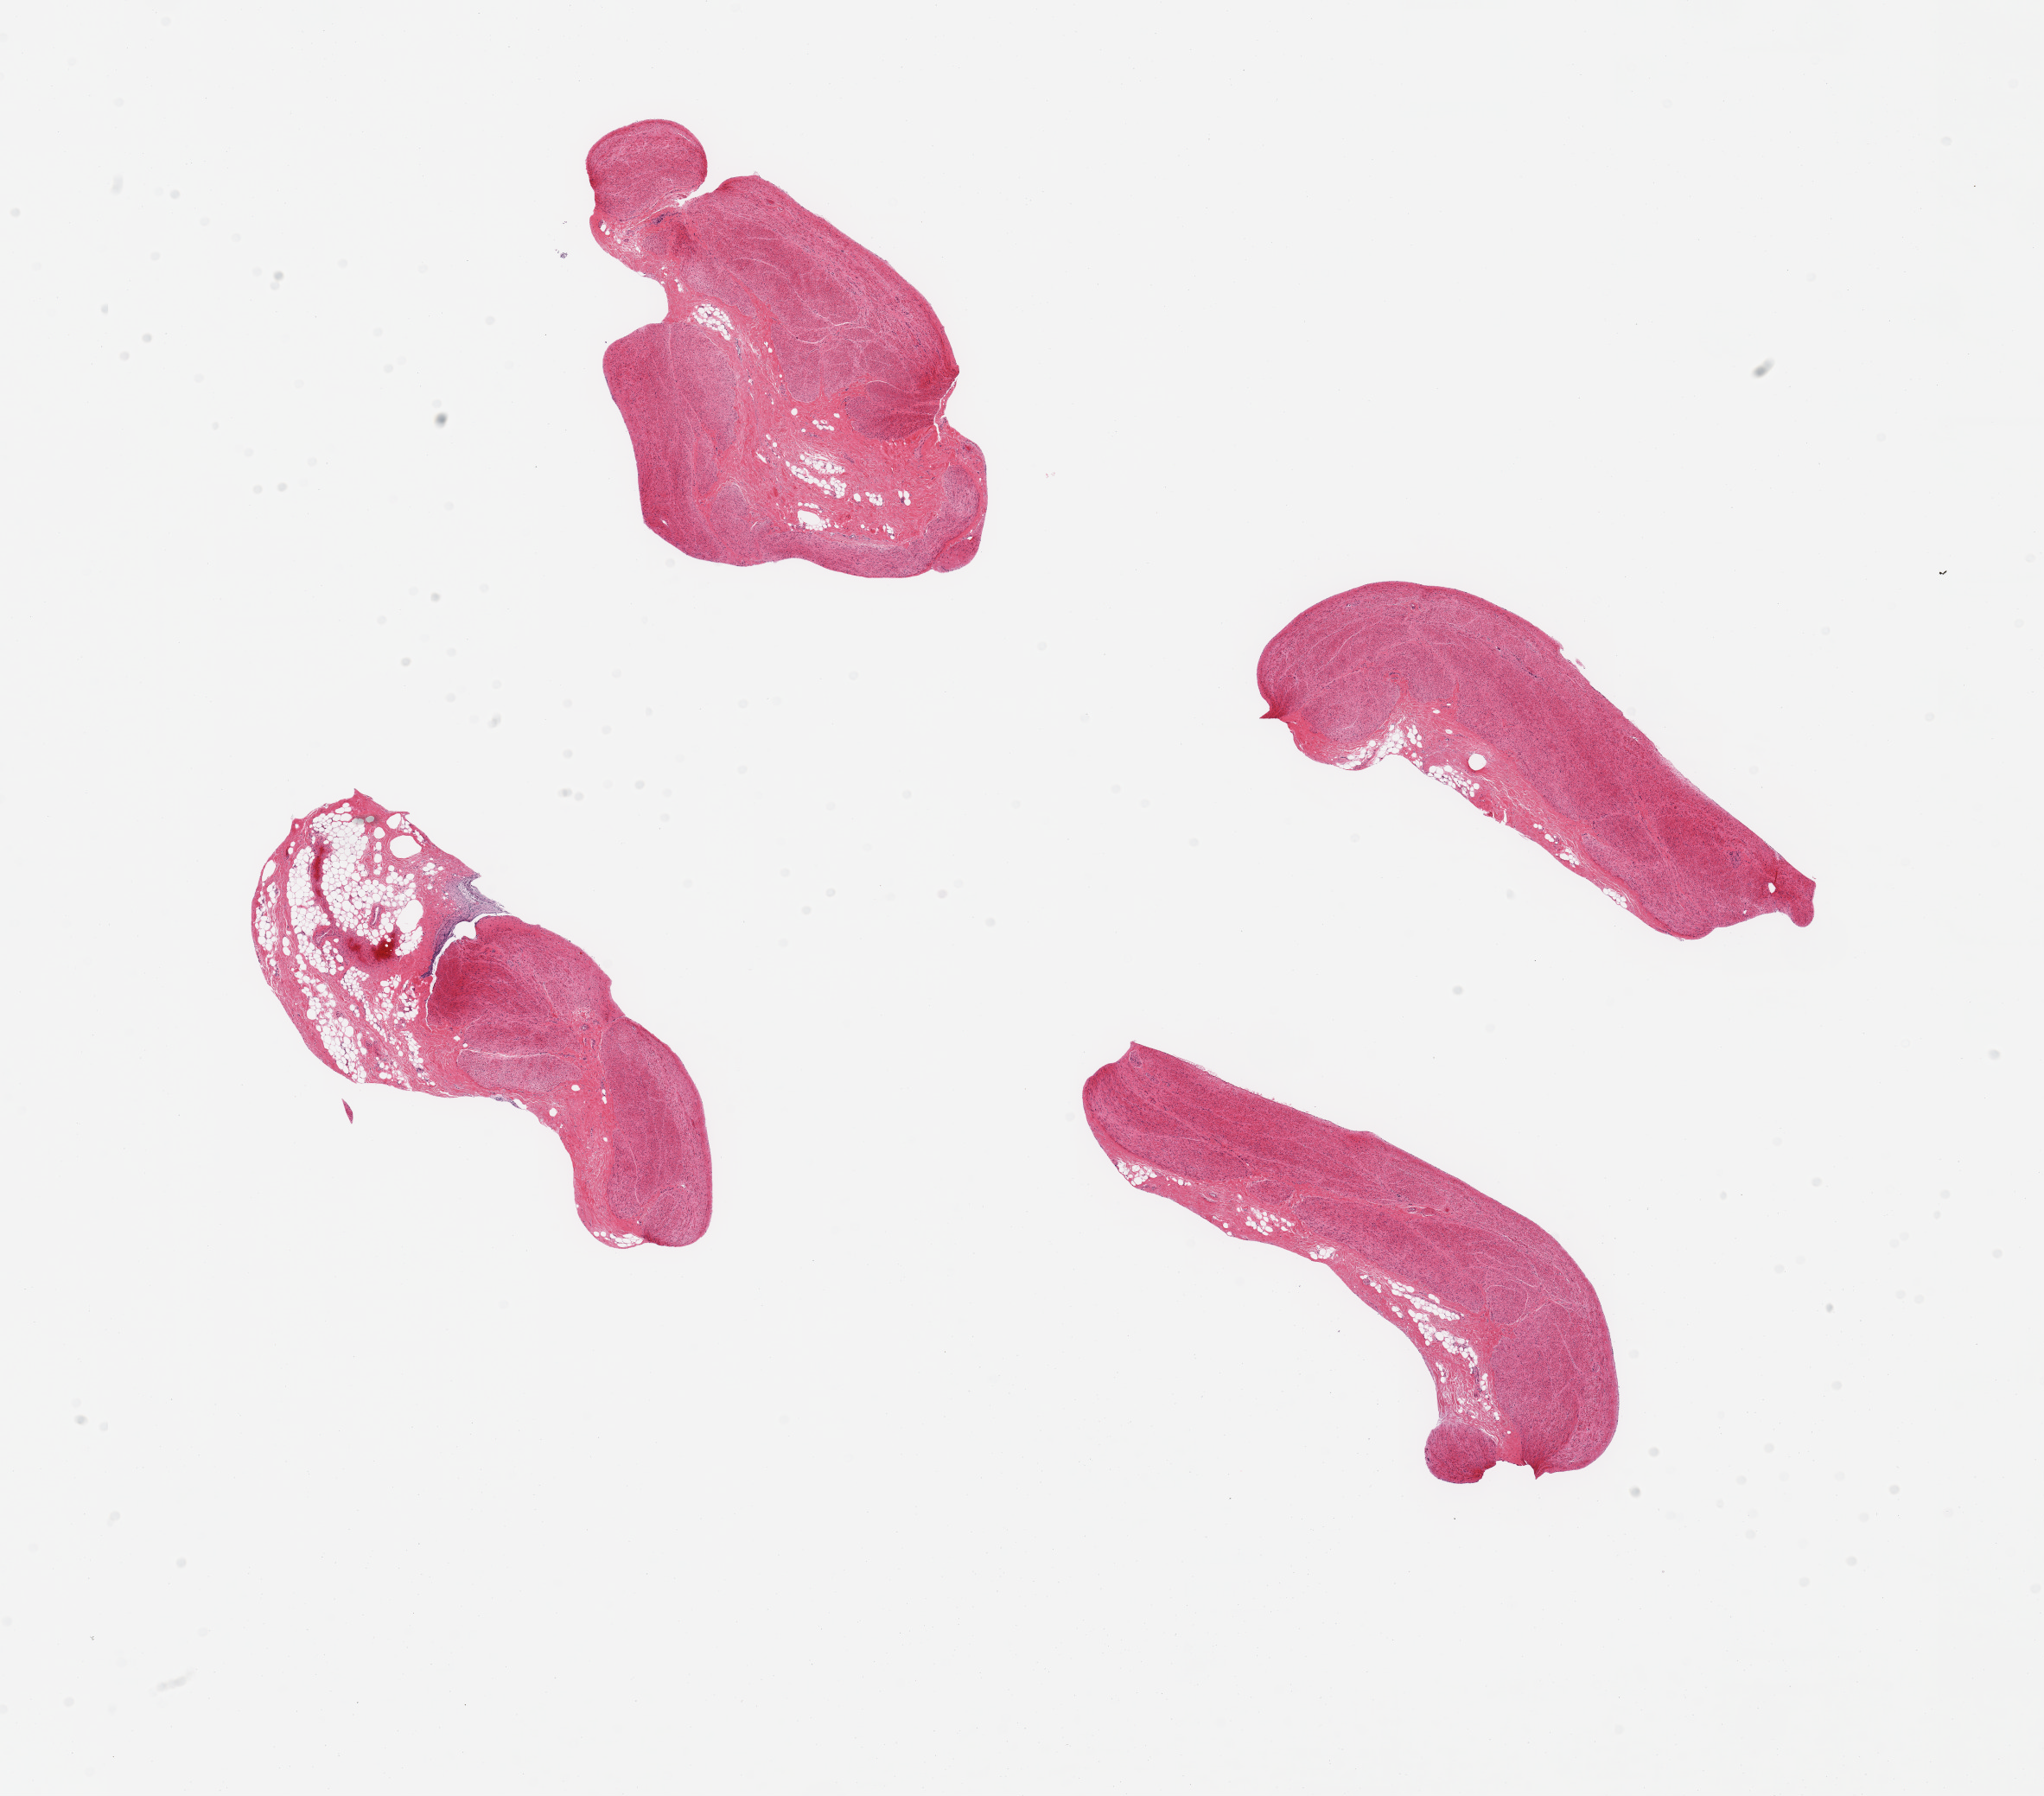
Hematoxylin and eosin (H&E) whole-slide image, brightfield — a low-resolution overview of the entire scanned area, about 18.7 x 16.4 mm (slide scanned at 20x); PAXgene-fixed, paraffin-embedded tissue; sampled site (target tissue): stomach; donor tissue sample. Donor sex: female.
* pathologist's review note for this sample: 4 pieces; no mucosa, only muscularis and fat